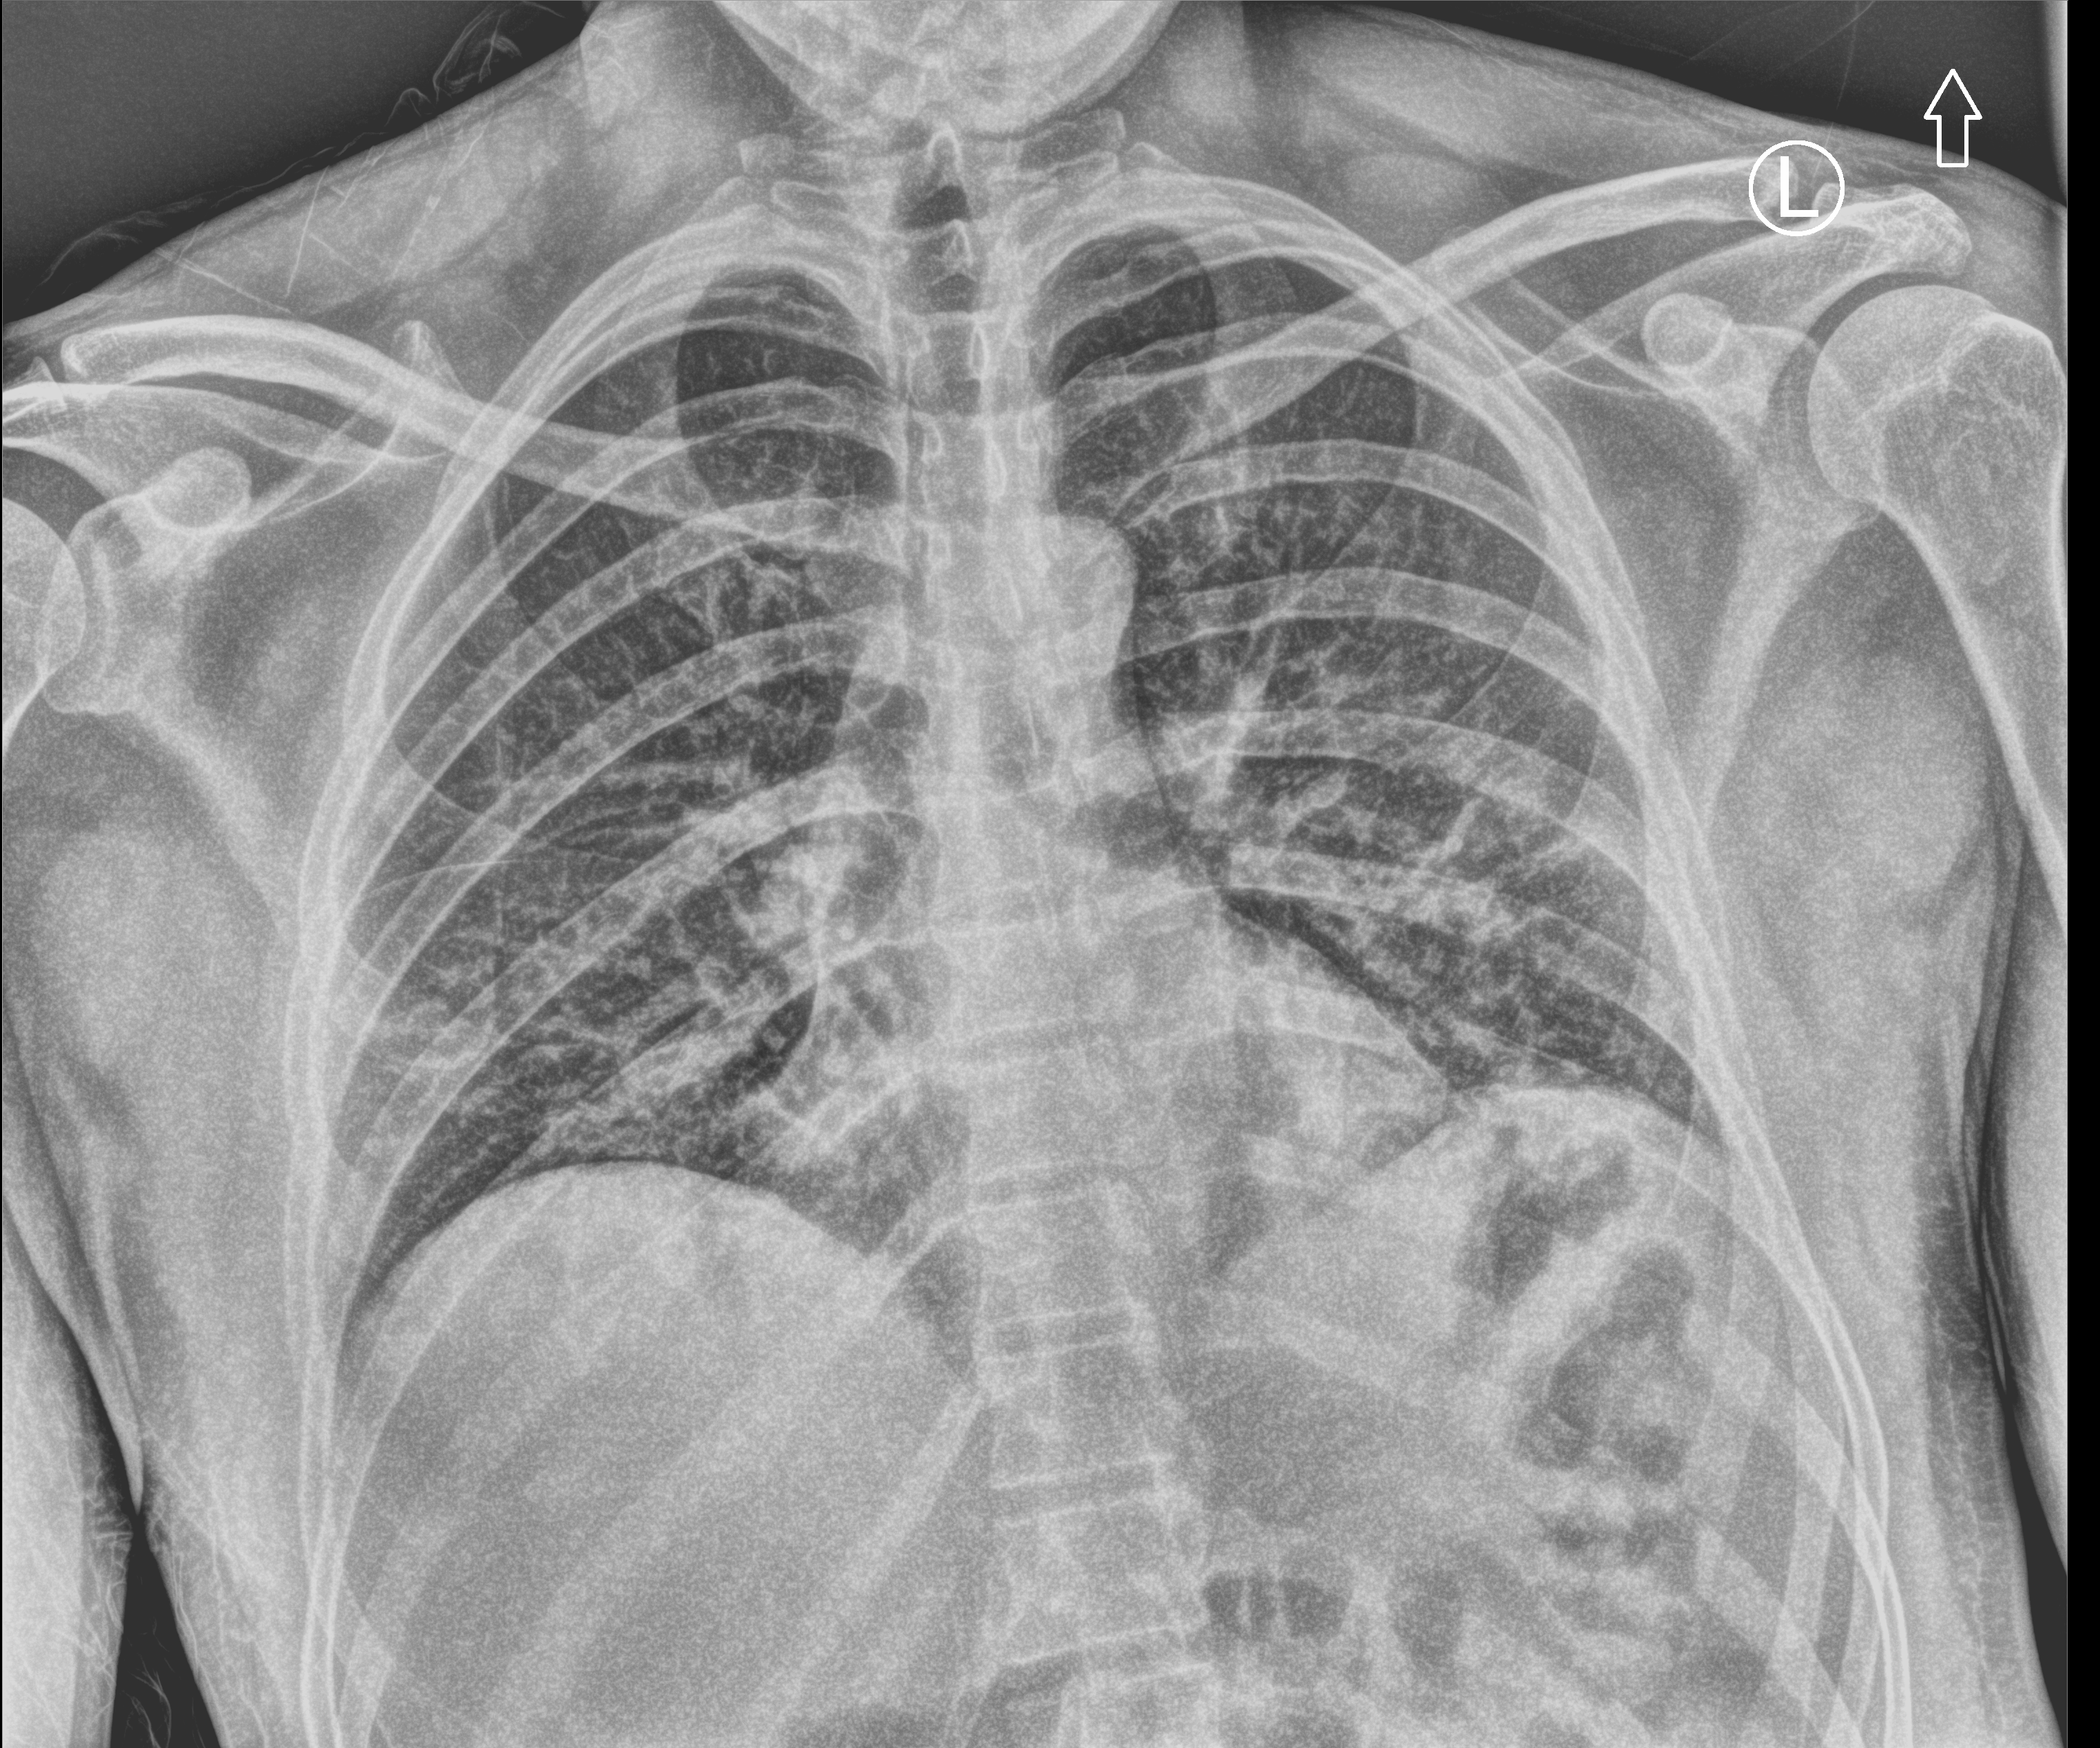
Chest X-ray (portable), anteroposterior (AP) projection. Male patient hospitalised with COVID-19, age 18–59 years.
From the hospital-stay record, not from the radiograph (when in the stay this image was taken is not recorded): diabetes (admission record): no.